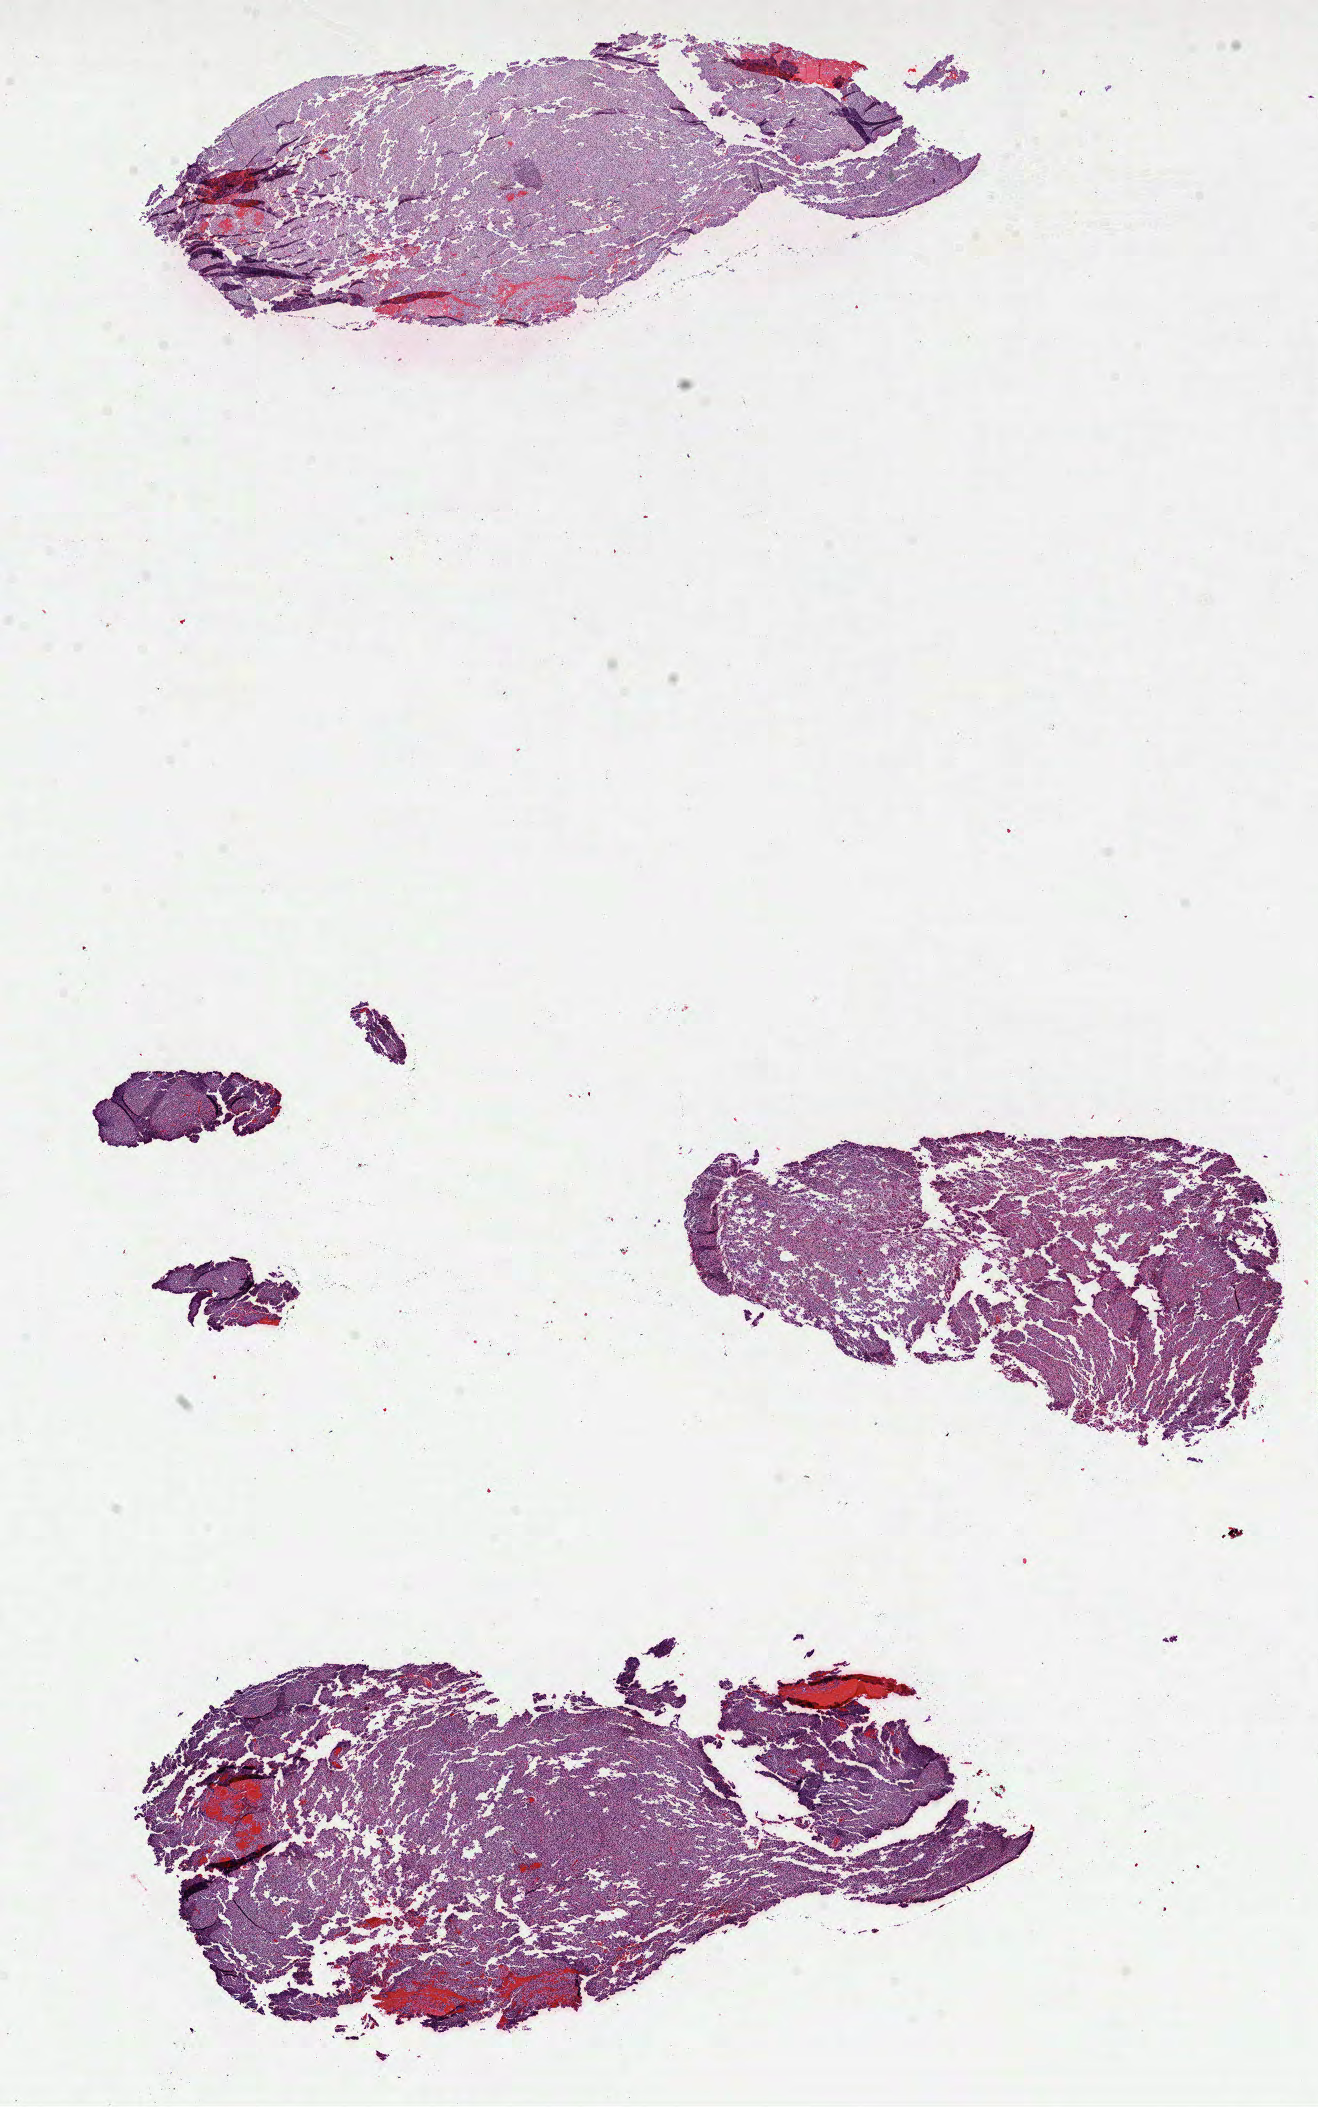
H&E-stained whole-slide image, a low-resolution overview of the entire scanned area, about 10.6 x 17.0 mm (slide scanned at 40x), formalin-fixed paraffin-embedded (FFPE) diagnostic section, sample: primary tumour, brain. Female, age 57 years at initial diagnosis. Histologic grade: G2 (moderately differentiated).
- histologic diagnosis: Oligodendroglioma, NOS